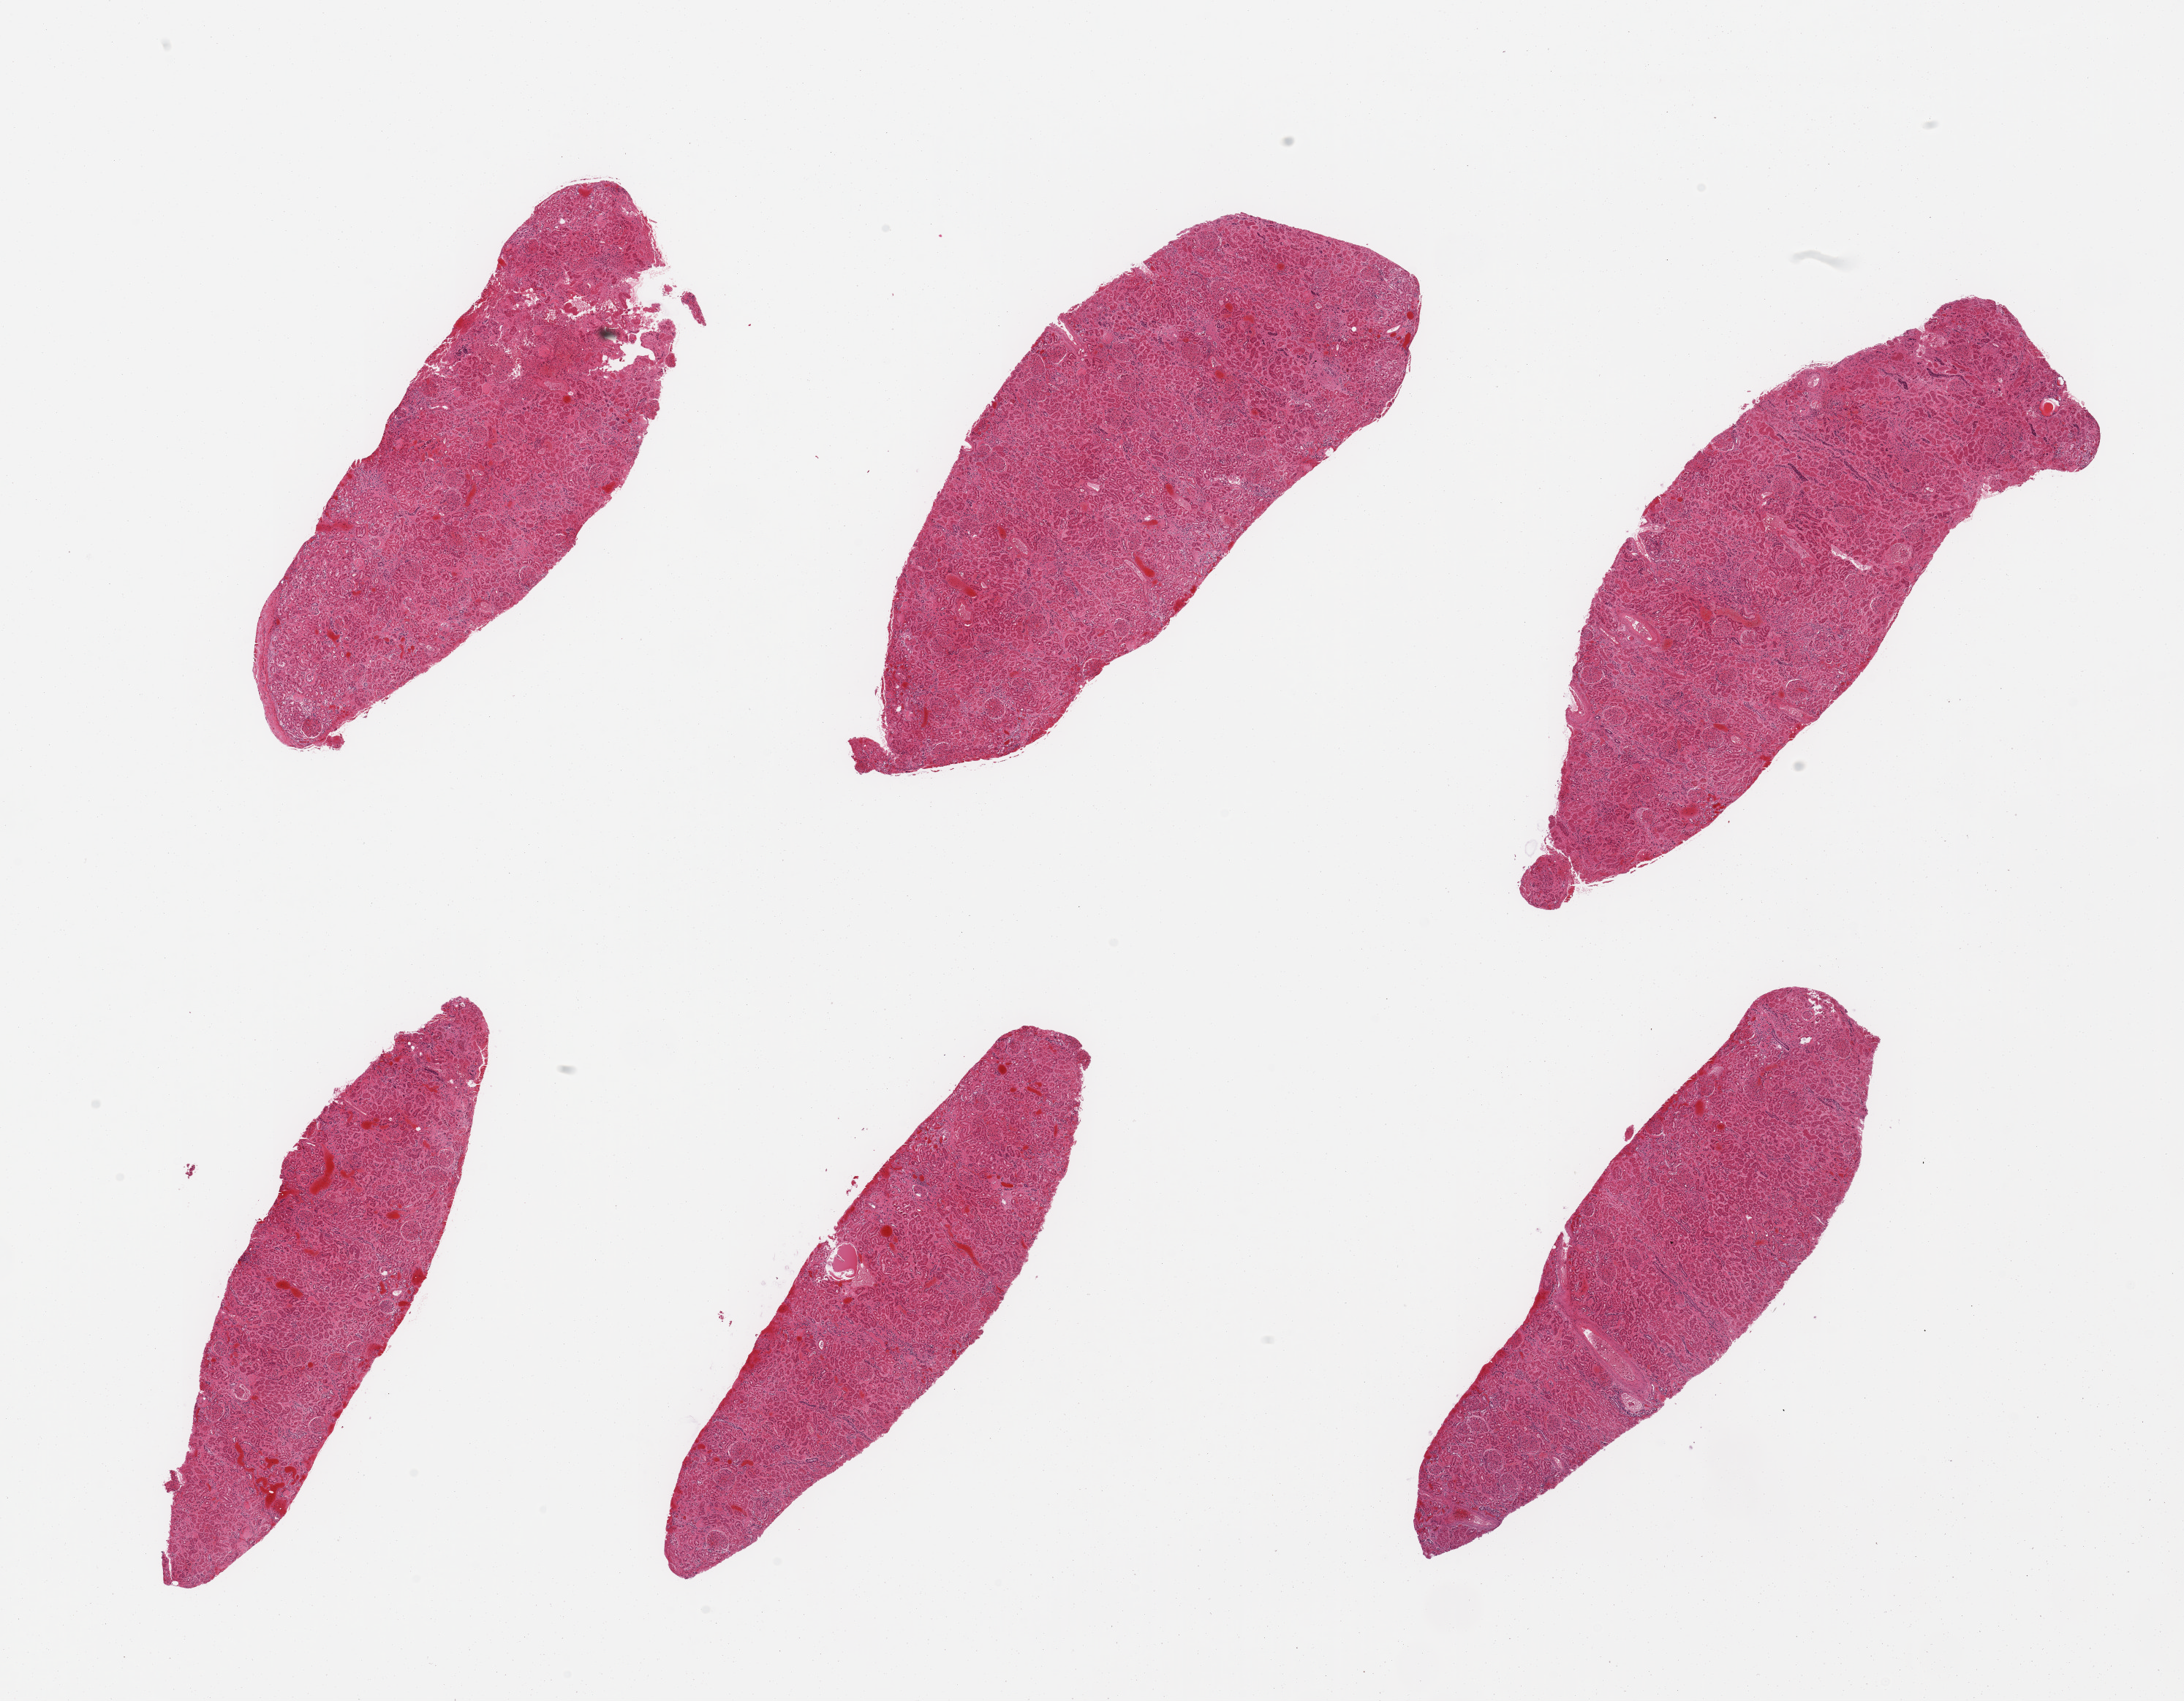
Digitized H&E-stained section — shown as a low-resolution overview of the whole scanned area (about 23.6 x 18.4 mm, slide scanned at 20x), PAXgene-fixed paraffin-embedded (PFPE) section, sampled site (target tissue): renal cortex, donor tissue sample. Donor sex: female.
Pathologist's review note for this sample: 6 pieces, glomeruli present; tubules with advanced autolysis.